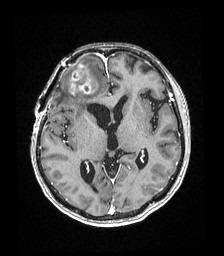
Brain MRI from a brain-tumour surgery series, one axial slice; T1-weighted post-contrast; 224 × 256 image matrix, field of view 219 × 250 mm. From the clinical record (not read from this slice): histopathology: Astrocytoma; WHO grade: 4; IDH mutation: yes.
Outlined on this slice (outlined manually by an expert reader):
- tumour: bounding box <71,64,97,95> (left, top, right, bottom; pixels)